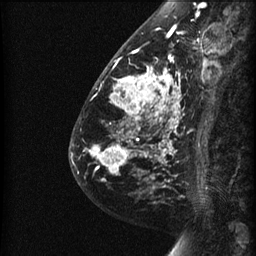
Breast MRI (dynamic contrast-enhanced), one sagittal slice. Position 20 of 60 along the scan axis. Dynamic contrast-enhanced series, image 2 of 3 at this slice position (ordered by acquisition). 1.5 T. TE 4.2 ms, TR 22.7 ms. 256 × 256 image matrix, field of view 180 × 180 mm. Female patient, age 48 years. Case-level facts recorded for this patient, not image findings: setting: breast cancer imaged before/during neoadjuvant chemotherapy; receptor status: triple-negative.
Outlined on this slice (semi-automatically segmented with operator editing):
- analysis volume of interest (the breast-tissue region the enhancement analysis was run in; not a lesion): bounding box (x1, y1, x2, y2) in pixels: (89, 27, 191, 180)
- tumour enhancement mask (voxels above the 90 % enhancement threshold inside the analysis volume of interest): (92, 27, 182, 174)